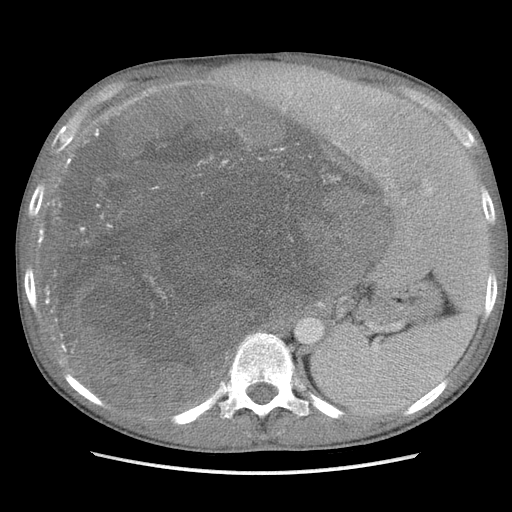
Contrast-enhanced abdominal CT, one axial slice; slice 76 of 115 in the series (ordered by position); soft-tissue window (W 400 / L 40 HU); 5 mm slice thickness; 512 × 512 image matrix, field of view 360 × 360 mm. Male patient. Case-level facts recorded for this patient, not image findings: diagnosis: adrenocortical carcinoma; tumour side: right adrenal; Ki-67 index: 13 %; stage (as recorded): 3.
Outlined on this slice (semi-automatically segmented with operator editing):
- mass: bounding box (x1, y1, x2, y2) in pixels: (56, 89, 381, 411)